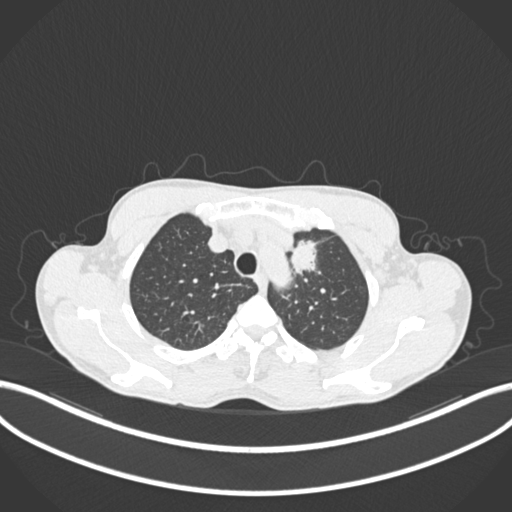
Chest CT, one axial slice; position 167 of 211 along the scan axis; reconstruction kernel B30f; 120 kVp; lung window (W 1500 / L -600 HU); 512 × 512 image matrix, field of view 400 × 400 mm. Patient: male, 58 years. Case-level facts recorded for this patient, not image findings: clinical TNM (as recorded): T1c N1 M0.
Outlined on this slice (bounding box drawn by a radiologist):
- lung tumour (recorded histology: adenocarcinoma): bounding box <286,232,321,283> (left, top, right, bottom; pixels)